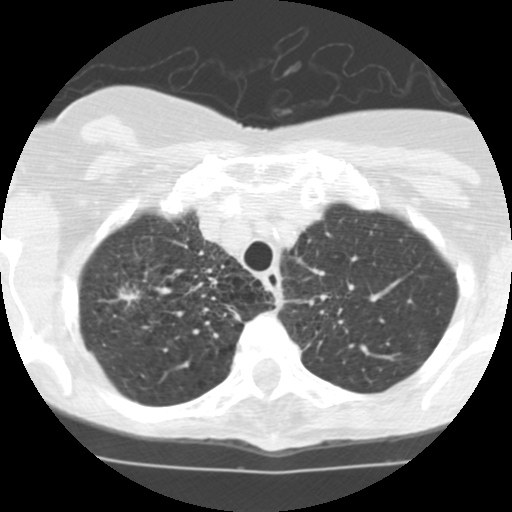
Low-dose screening chest CT, one axial slice. Position 94 of 115 along the scan axis. Lung window (W 1500 / L -600 HU). 2.5 mm slice thickness. 512 × 512 image matrix, field of view 280 × 280 mm.
Annotated regions visible in this slice (outlined manually by an expert reader):
- lesion 1 (tumor, upper lobe of right lung): box from (x=118, y=288) to (x=140, y=304) px